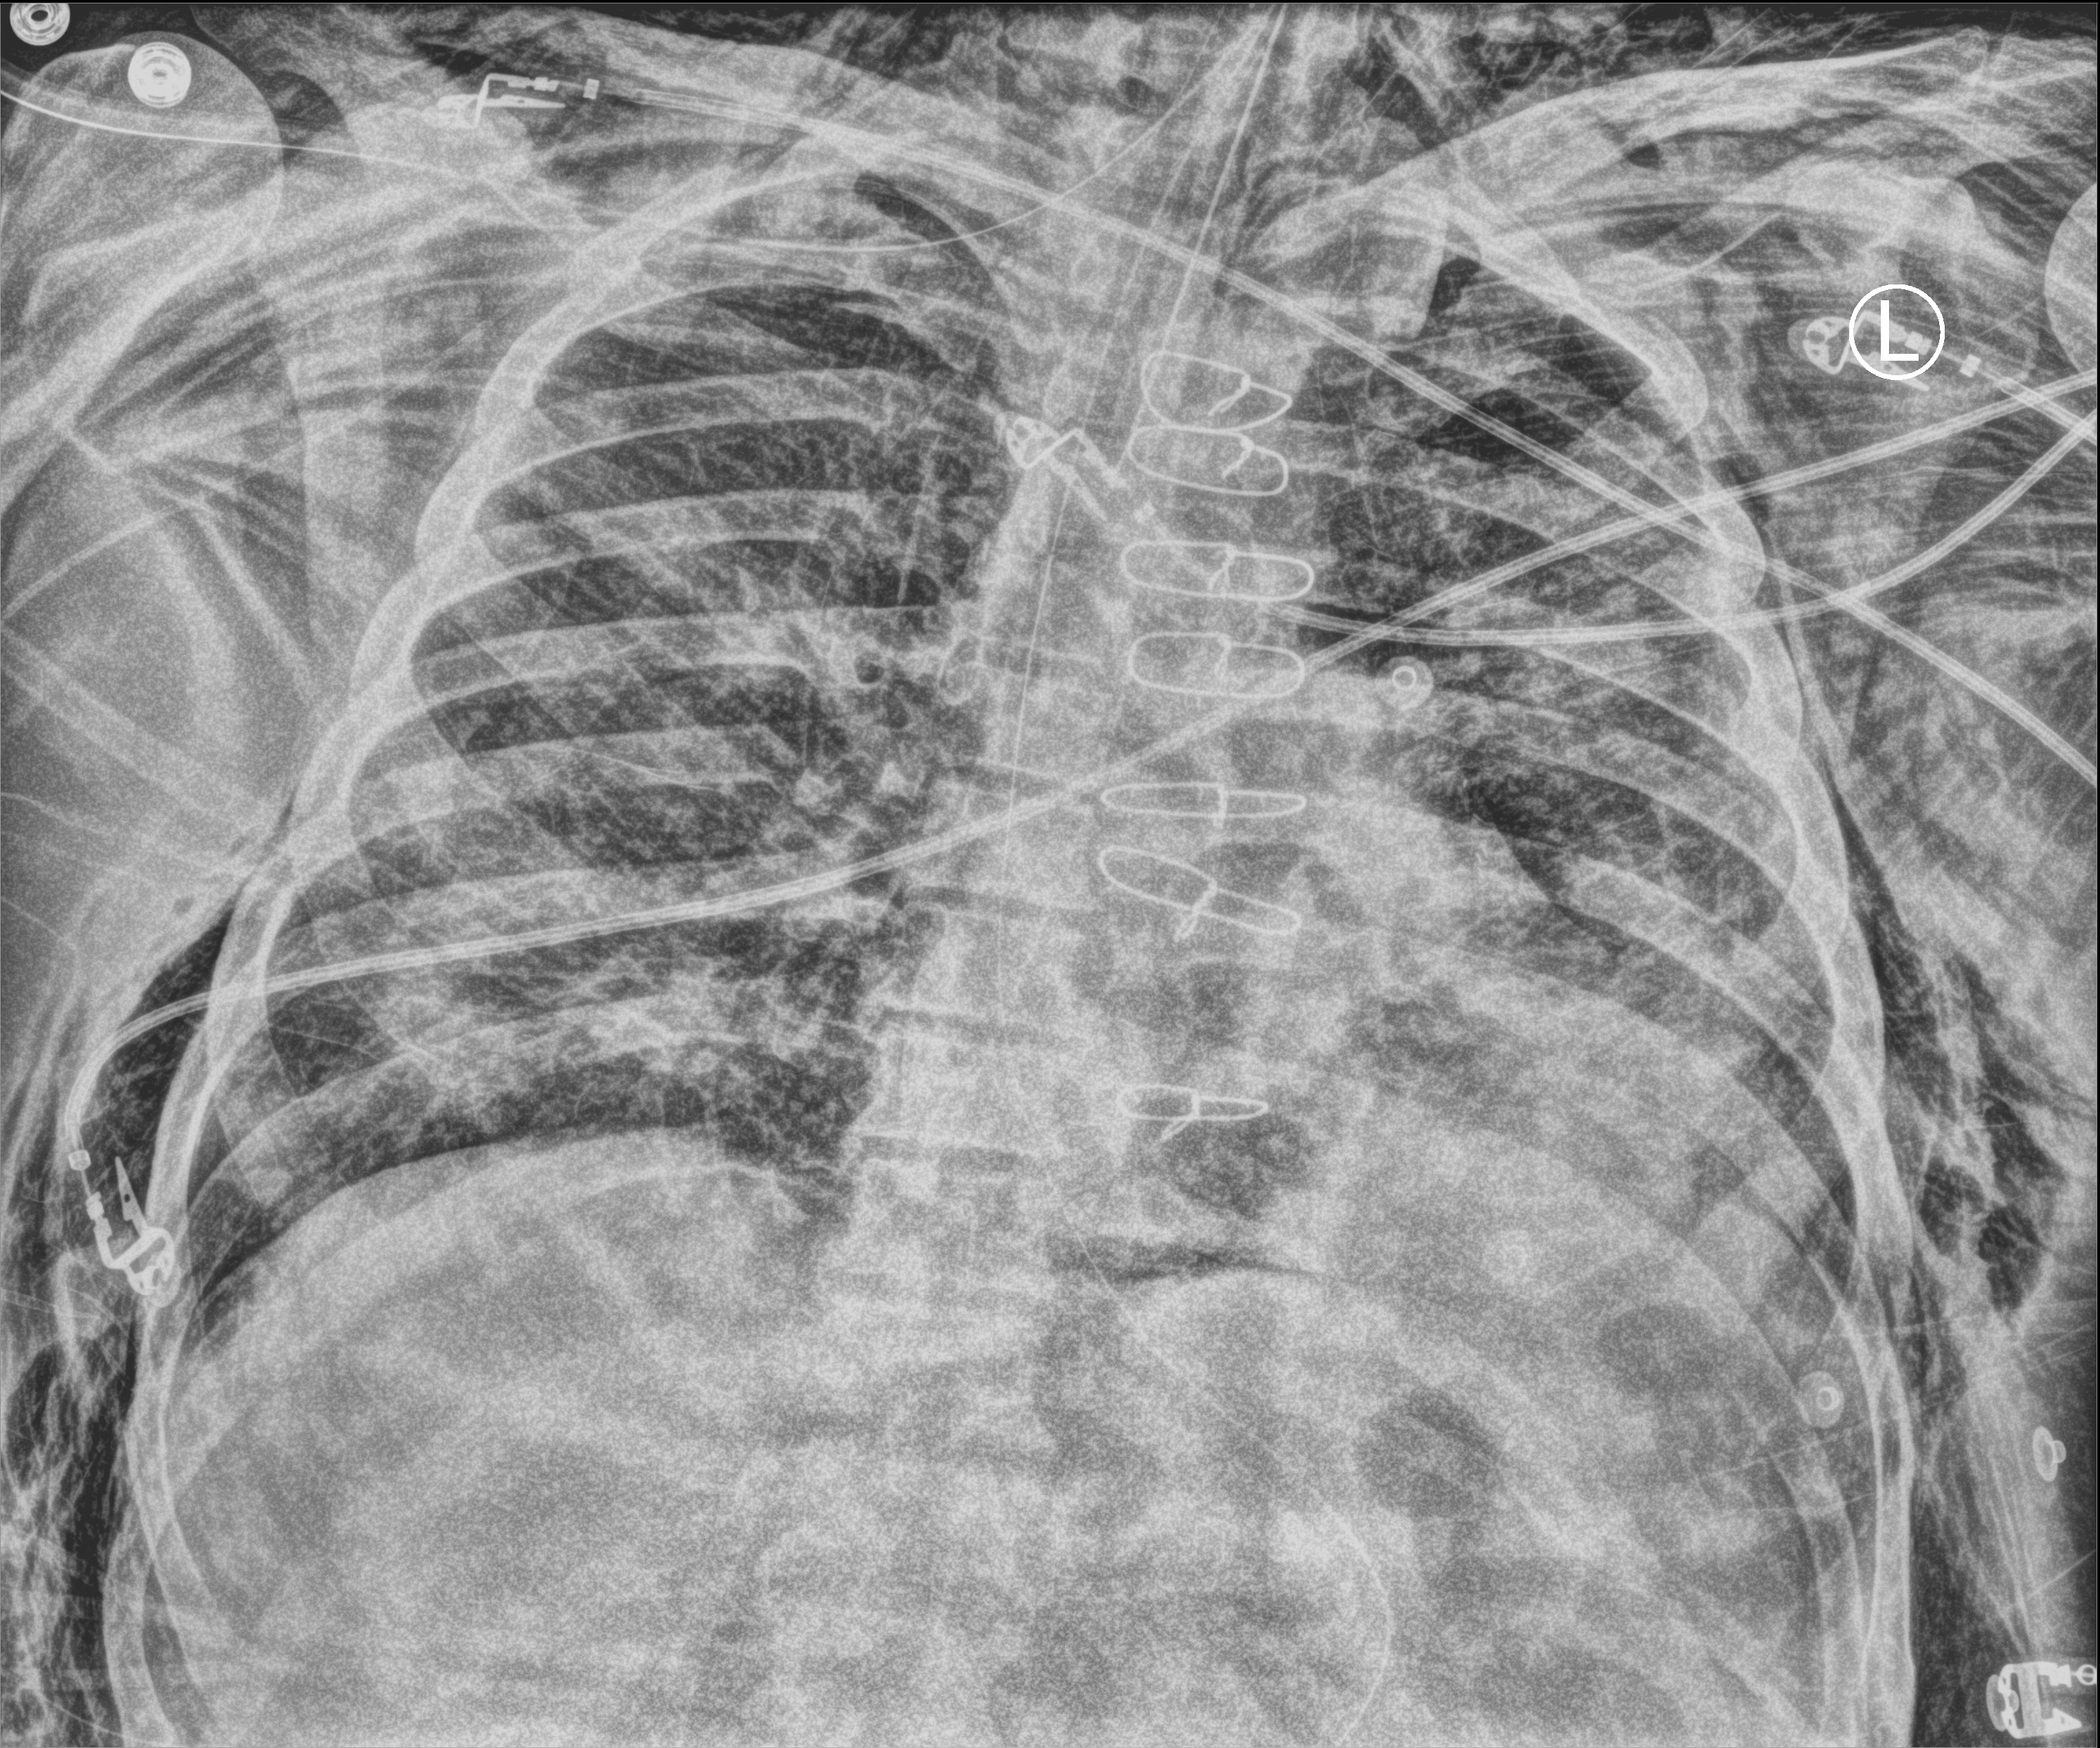
Portable chest radiograph, anteroposterior (AP) projection. Male patient hospitalised with COVID-19, age 60–74 years.
Hospital-stay facts (about this admission, not read from this image; timing relative to this image not recorded):
- admitted to intensive care during this hospital stay: yes